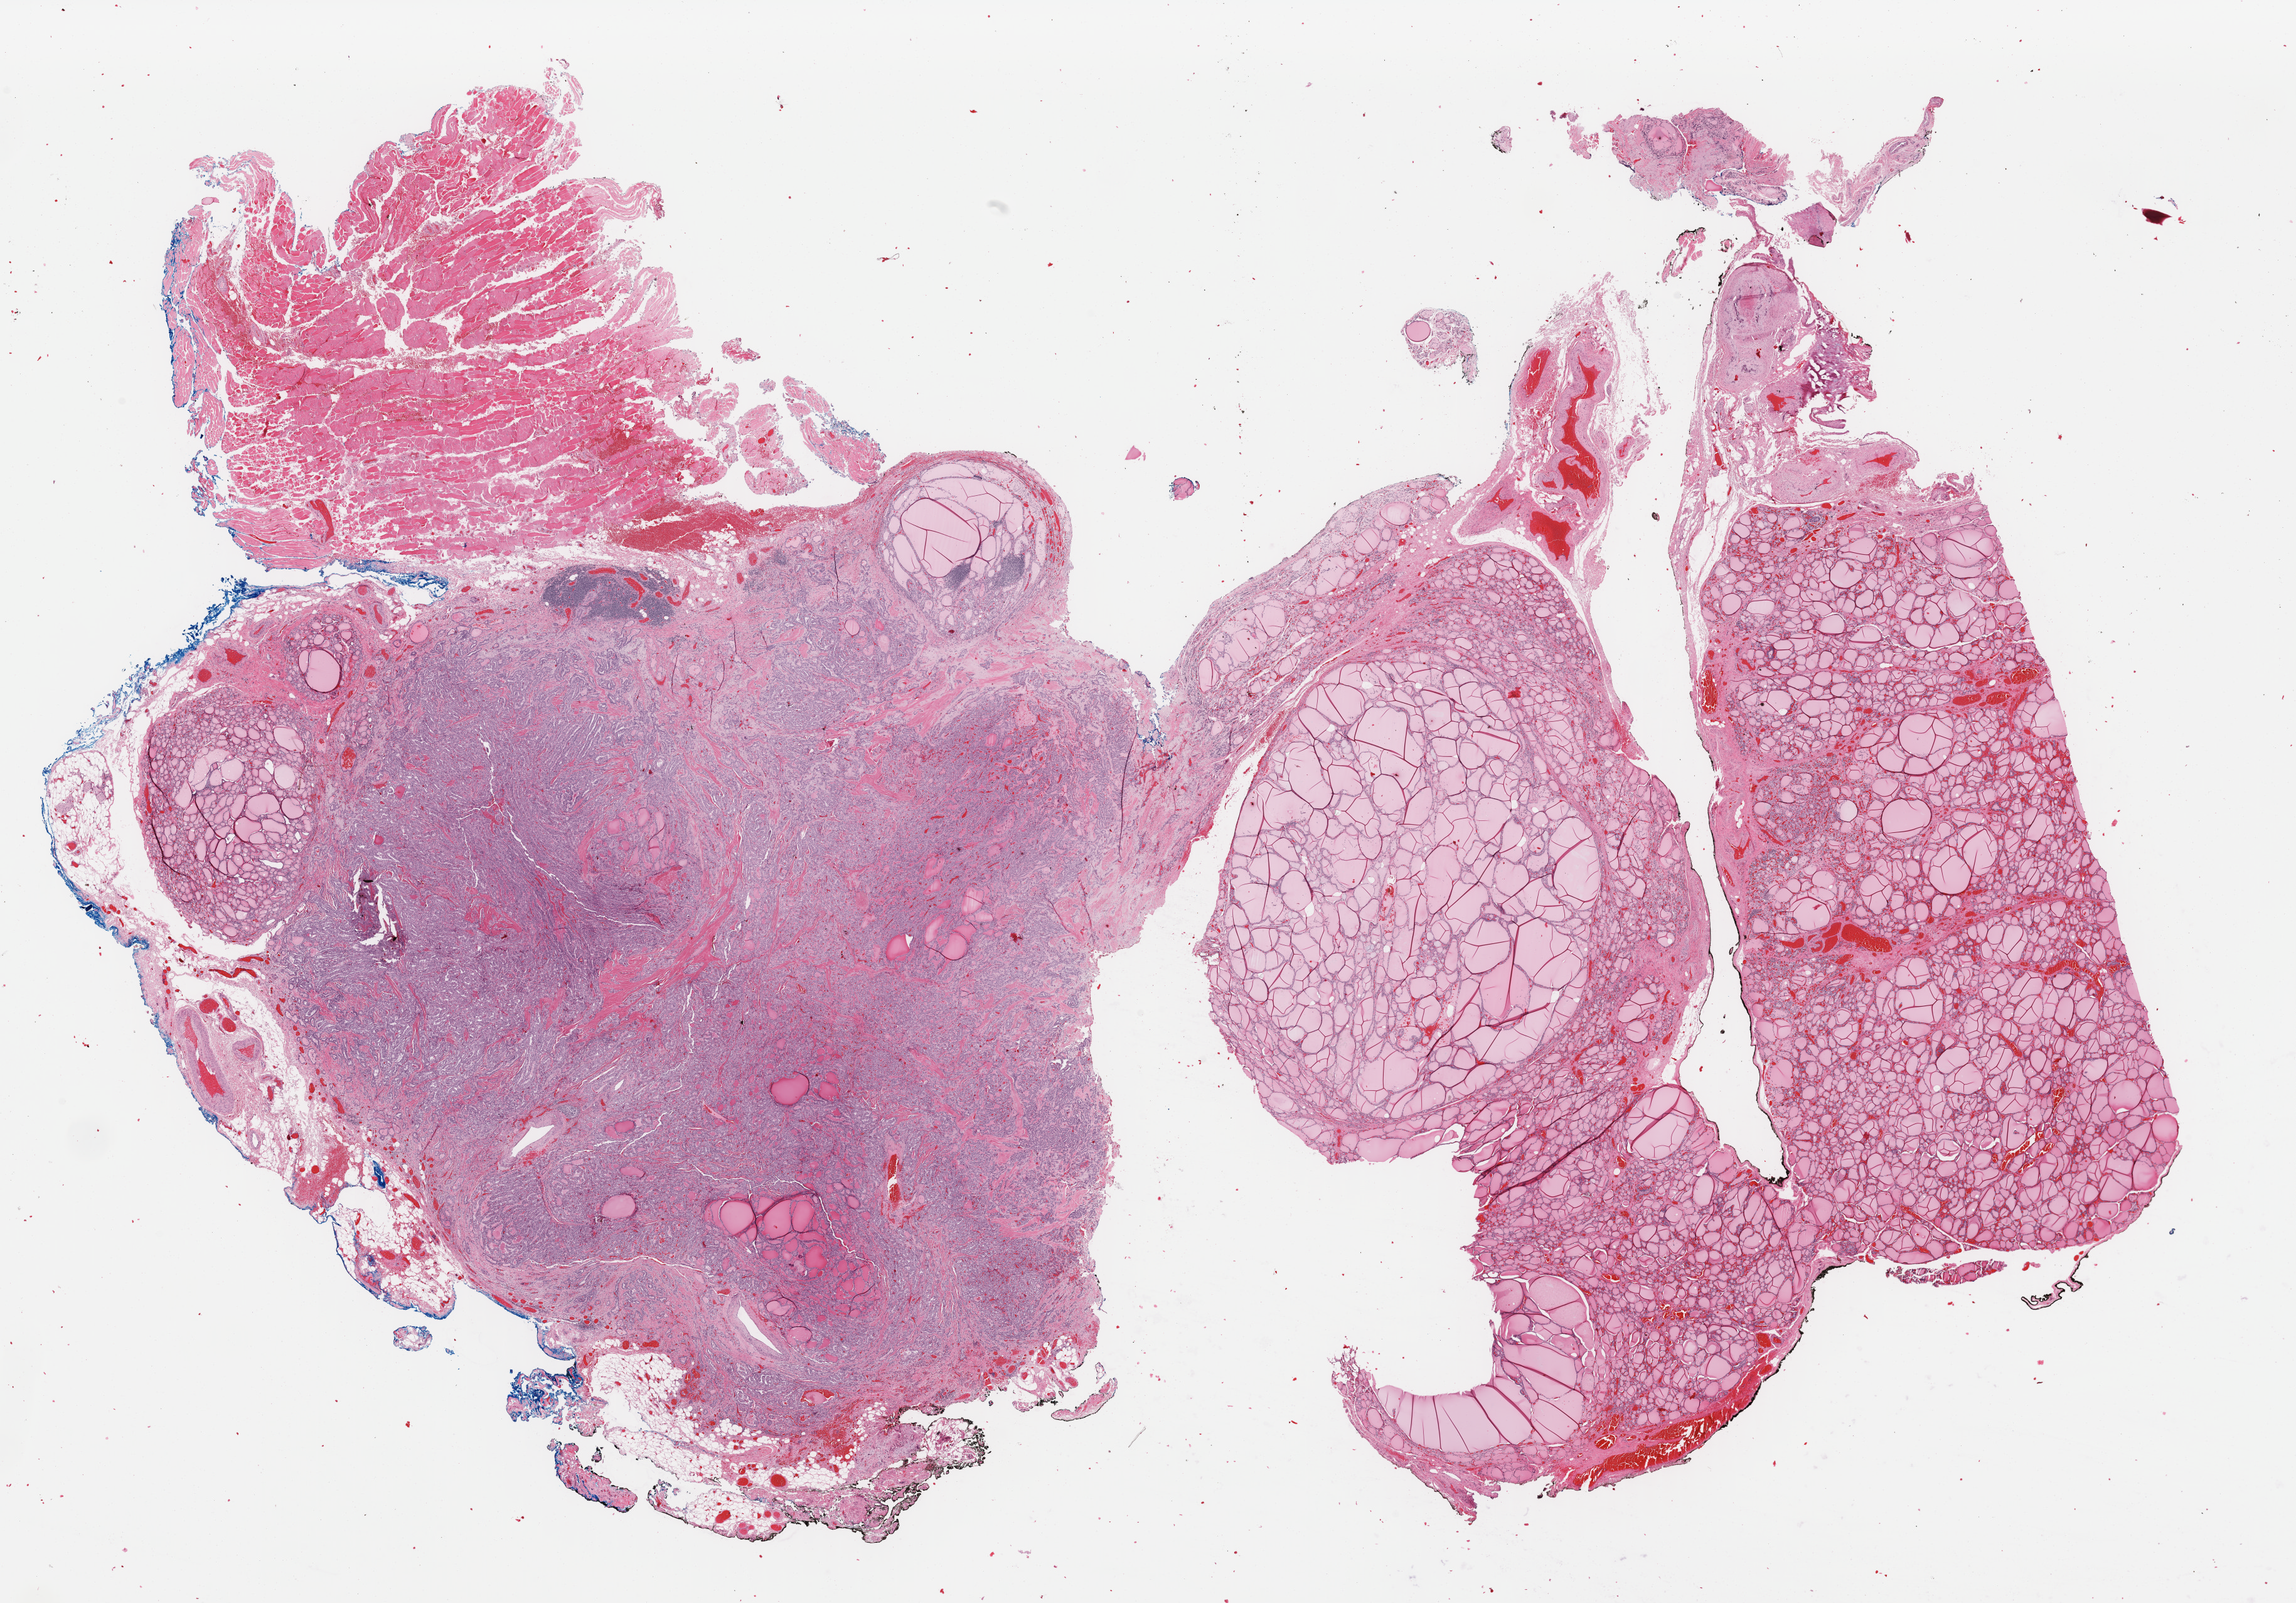
H&E-stained whole-slide image — low-resolution overview of the scanned area, about 28.9 x 20.1 mm (from a 40x scan), formalin-fixed paraffin-embedded (FFPE) diagnostic section, sample: primary tumour, thyroid. Female, age 76 years at initial diagnosis.
Laterality: right. Diagnosis: Papillary carcinoma, columnar cell (thyroid gland). TNM: T3 N0 M0. Lymph nodes positive (case pathology): 0 of 1 examined. AJCC pathologic stage: III (7th edition).